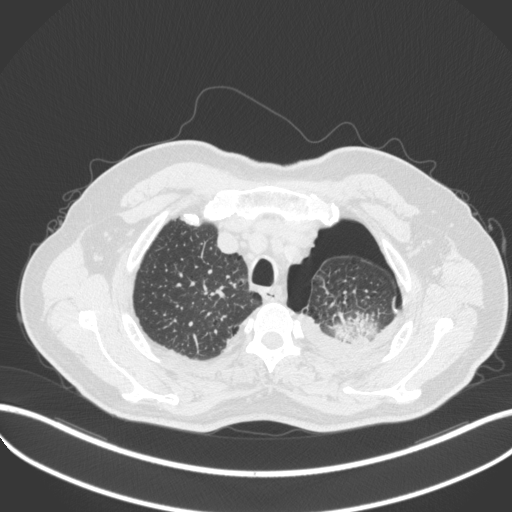
Chest CT, one axial slice. Slice 418 of 466 in the series (ordered by position). 120 kVp. Lung window (W 1500 / L -600 HU). 1 mm slice thickness. 512 × 512 image matrix. Male patient, age 76 years. Case-level facts recorded for this patient, not image findings: clinical TNM (as recorded): T3 N0 M1b.
Outlined on this slice (bounding box drawn by a radiologist):
- lung tumour (recorded histology: adenocarcinoma): bounding box [x1, y1, x2, y2] px = [330, 314, 381, 347]